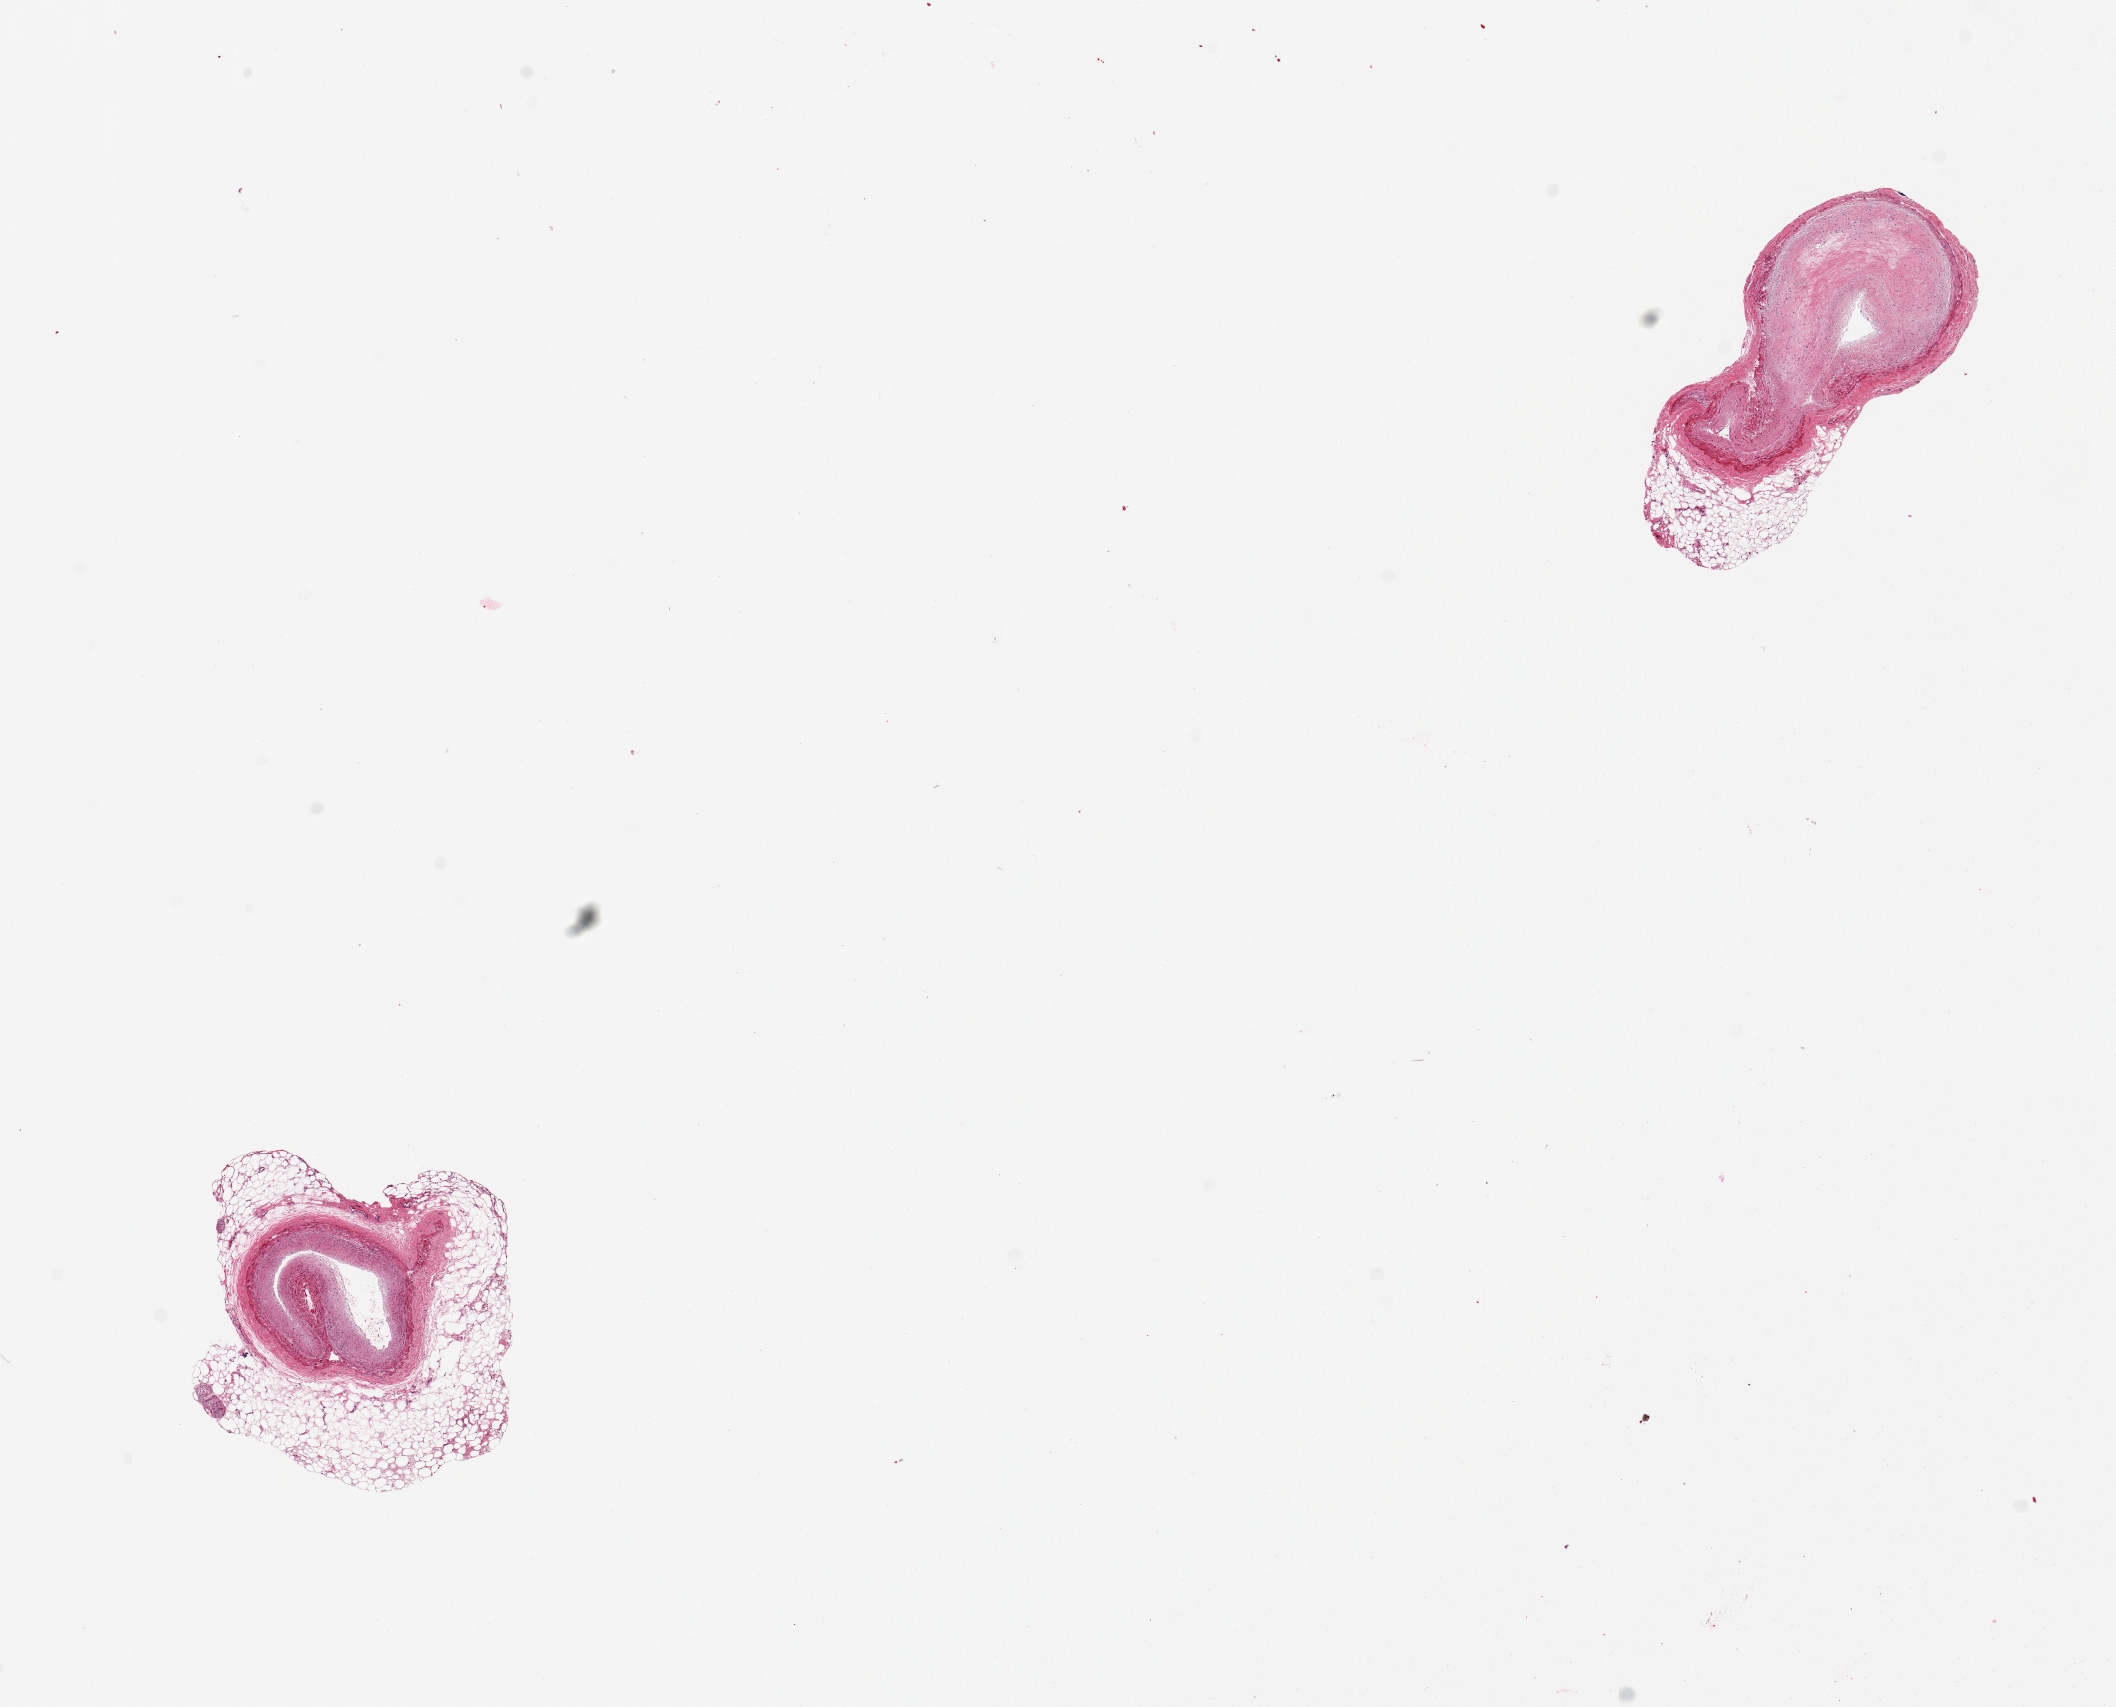
Whole-slide image, haematoxylin and eosin stain, brightfield — a low-resolution overview of the entire scanned area, about 16.7 x 13.5 mm; PAXgene-fixed, paraffin-embedded tissue; section of coronary artery (target tissue); donor tissue sample. Donor: male.
• review note (as recorded): 2 pieces, 3x1.5 and 2.5x2mm; subtotally occlusive atherosis, ave d. ~2mm. Adherent fat, disccontinuous, on both, ~0.5mm